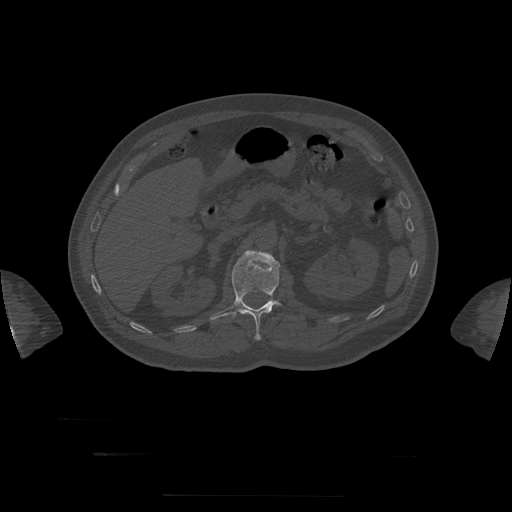
CT including the spine, one axial slice; slice 47 of 397 in the series (ordered by position); 120 kVp; bone window (W 1800 / L 400 HU); 1.25 mm slice thickness; 512 × 512 image matrix. Patient age 73 years. Case-level facts recorded for this patient, not image findings: primary cancer: prostate.
Structures marked on this image (semi-automatic segmentation, software-assisted and operator-edited):
- L1 vertebra: bounding box [x1, y1, x2, y2] px = [210, 251, 282, 340]